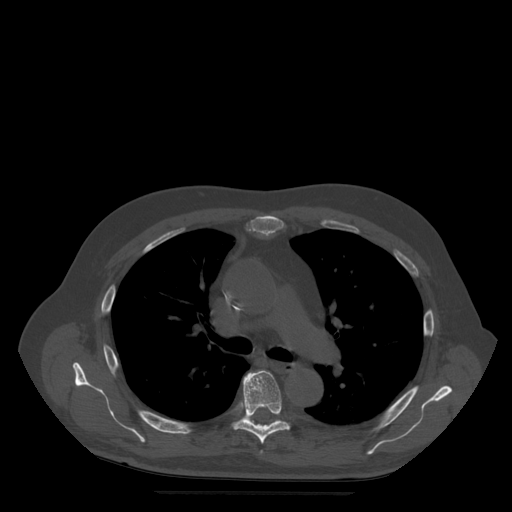
CT including the spine, one axial slice; bone window (W 1800 / L 400 HU); 1.25 mm slice thickness; 512 × 512 image matrix. Patient age 72 years. Case-level facts recorded for this patient, not image findings: primary cancer: prostate.
Annotated regions visible in this slice (semi-automatic segmentation, software-assisted and operator-edited):
- T6 vertebra: bounding box <232,371,291,444> (left, top, right, bottom; pixels)
- T7 vertebra: <249,419,277,424>